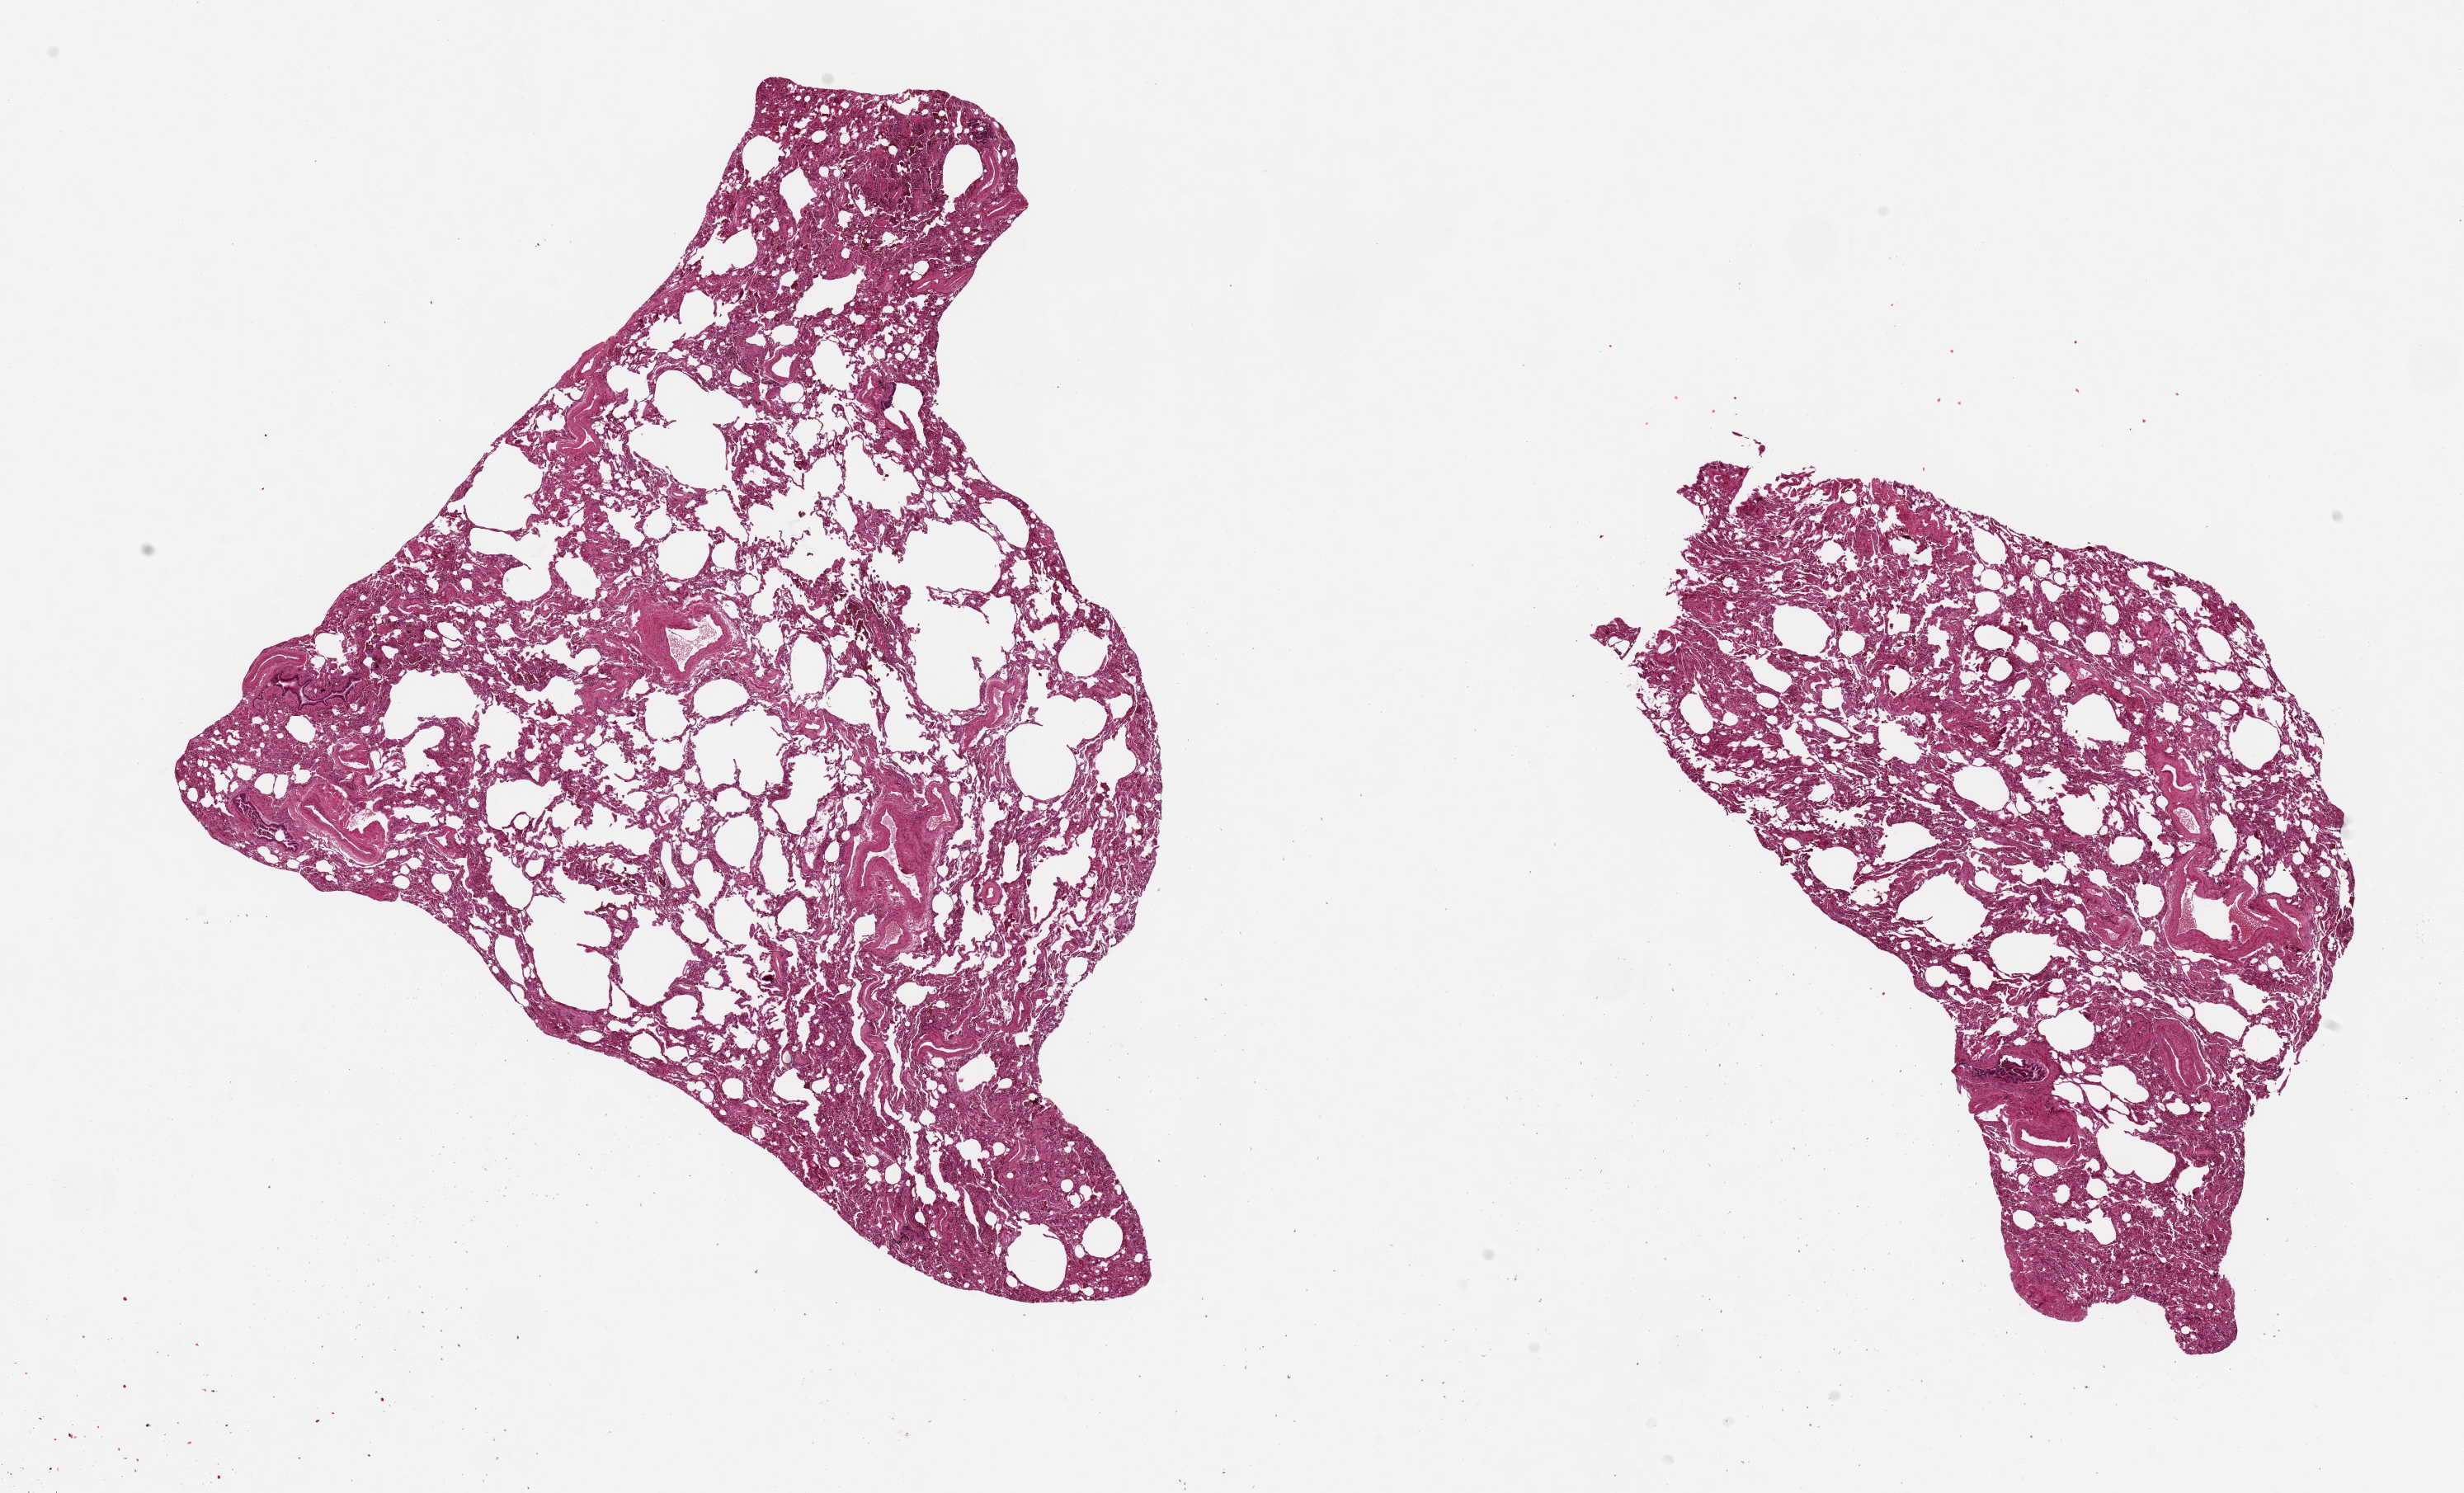
Whole-slide image, haematoxylin and eosin stain — shown as a low-resolution overview of the whole scanned area (about 23.6 x 14.3 mm, from a 20x scan); PAXgene-fixed paraffin-embedded (PFPE) section; target tissue: lung; tissue donor sample.
• reviewer comment on this tissue sample: 2 aliquots. DAD type changes and alveolar congestion present